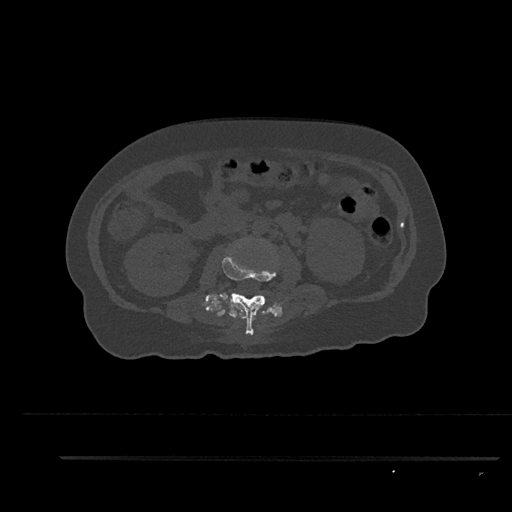
CT including the spine, one axial slice; position 135 of 797 along the scan axis; bone window (W 1800 / L 400 HU); 512 × 512 image matrix, field of view 408 × 408 mm. Patient: female, 44 years. Case-level facts recorded for this patient, not image findings: primary cancer: renal; vertebrae with lytic lesions (as recorded): L1.
Outlined on this slice (semi-automatic segmentation, software-assisted and operator-edited):
- L2 vertebra: bounding box [x1, y1, x2, y2] px = [222, 250, 276, 335]